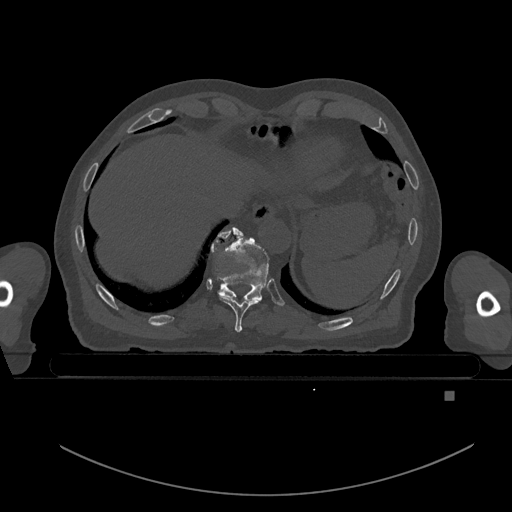
CT including the spine, one axial slice. Position 118 of 969 along the scan axis. Bone window (W 1800 / L 400 HU). 0.5 mm slice thickness. 512 × 512 image matrix. Patient: male, 82 years. From the clinical record (not read from this slice): primary cancer: prostate; vertebrae with lytic lesions (as recorded): T11, T9, T8, T2.
Structures marked on this image (semi-automatically segmented with operator editing):
- T10 vertebra: box from (x=211, y=227) to (x=269, y=301) px
- T9 vertebra: (x=218, y=230)–(x=261, y=332)